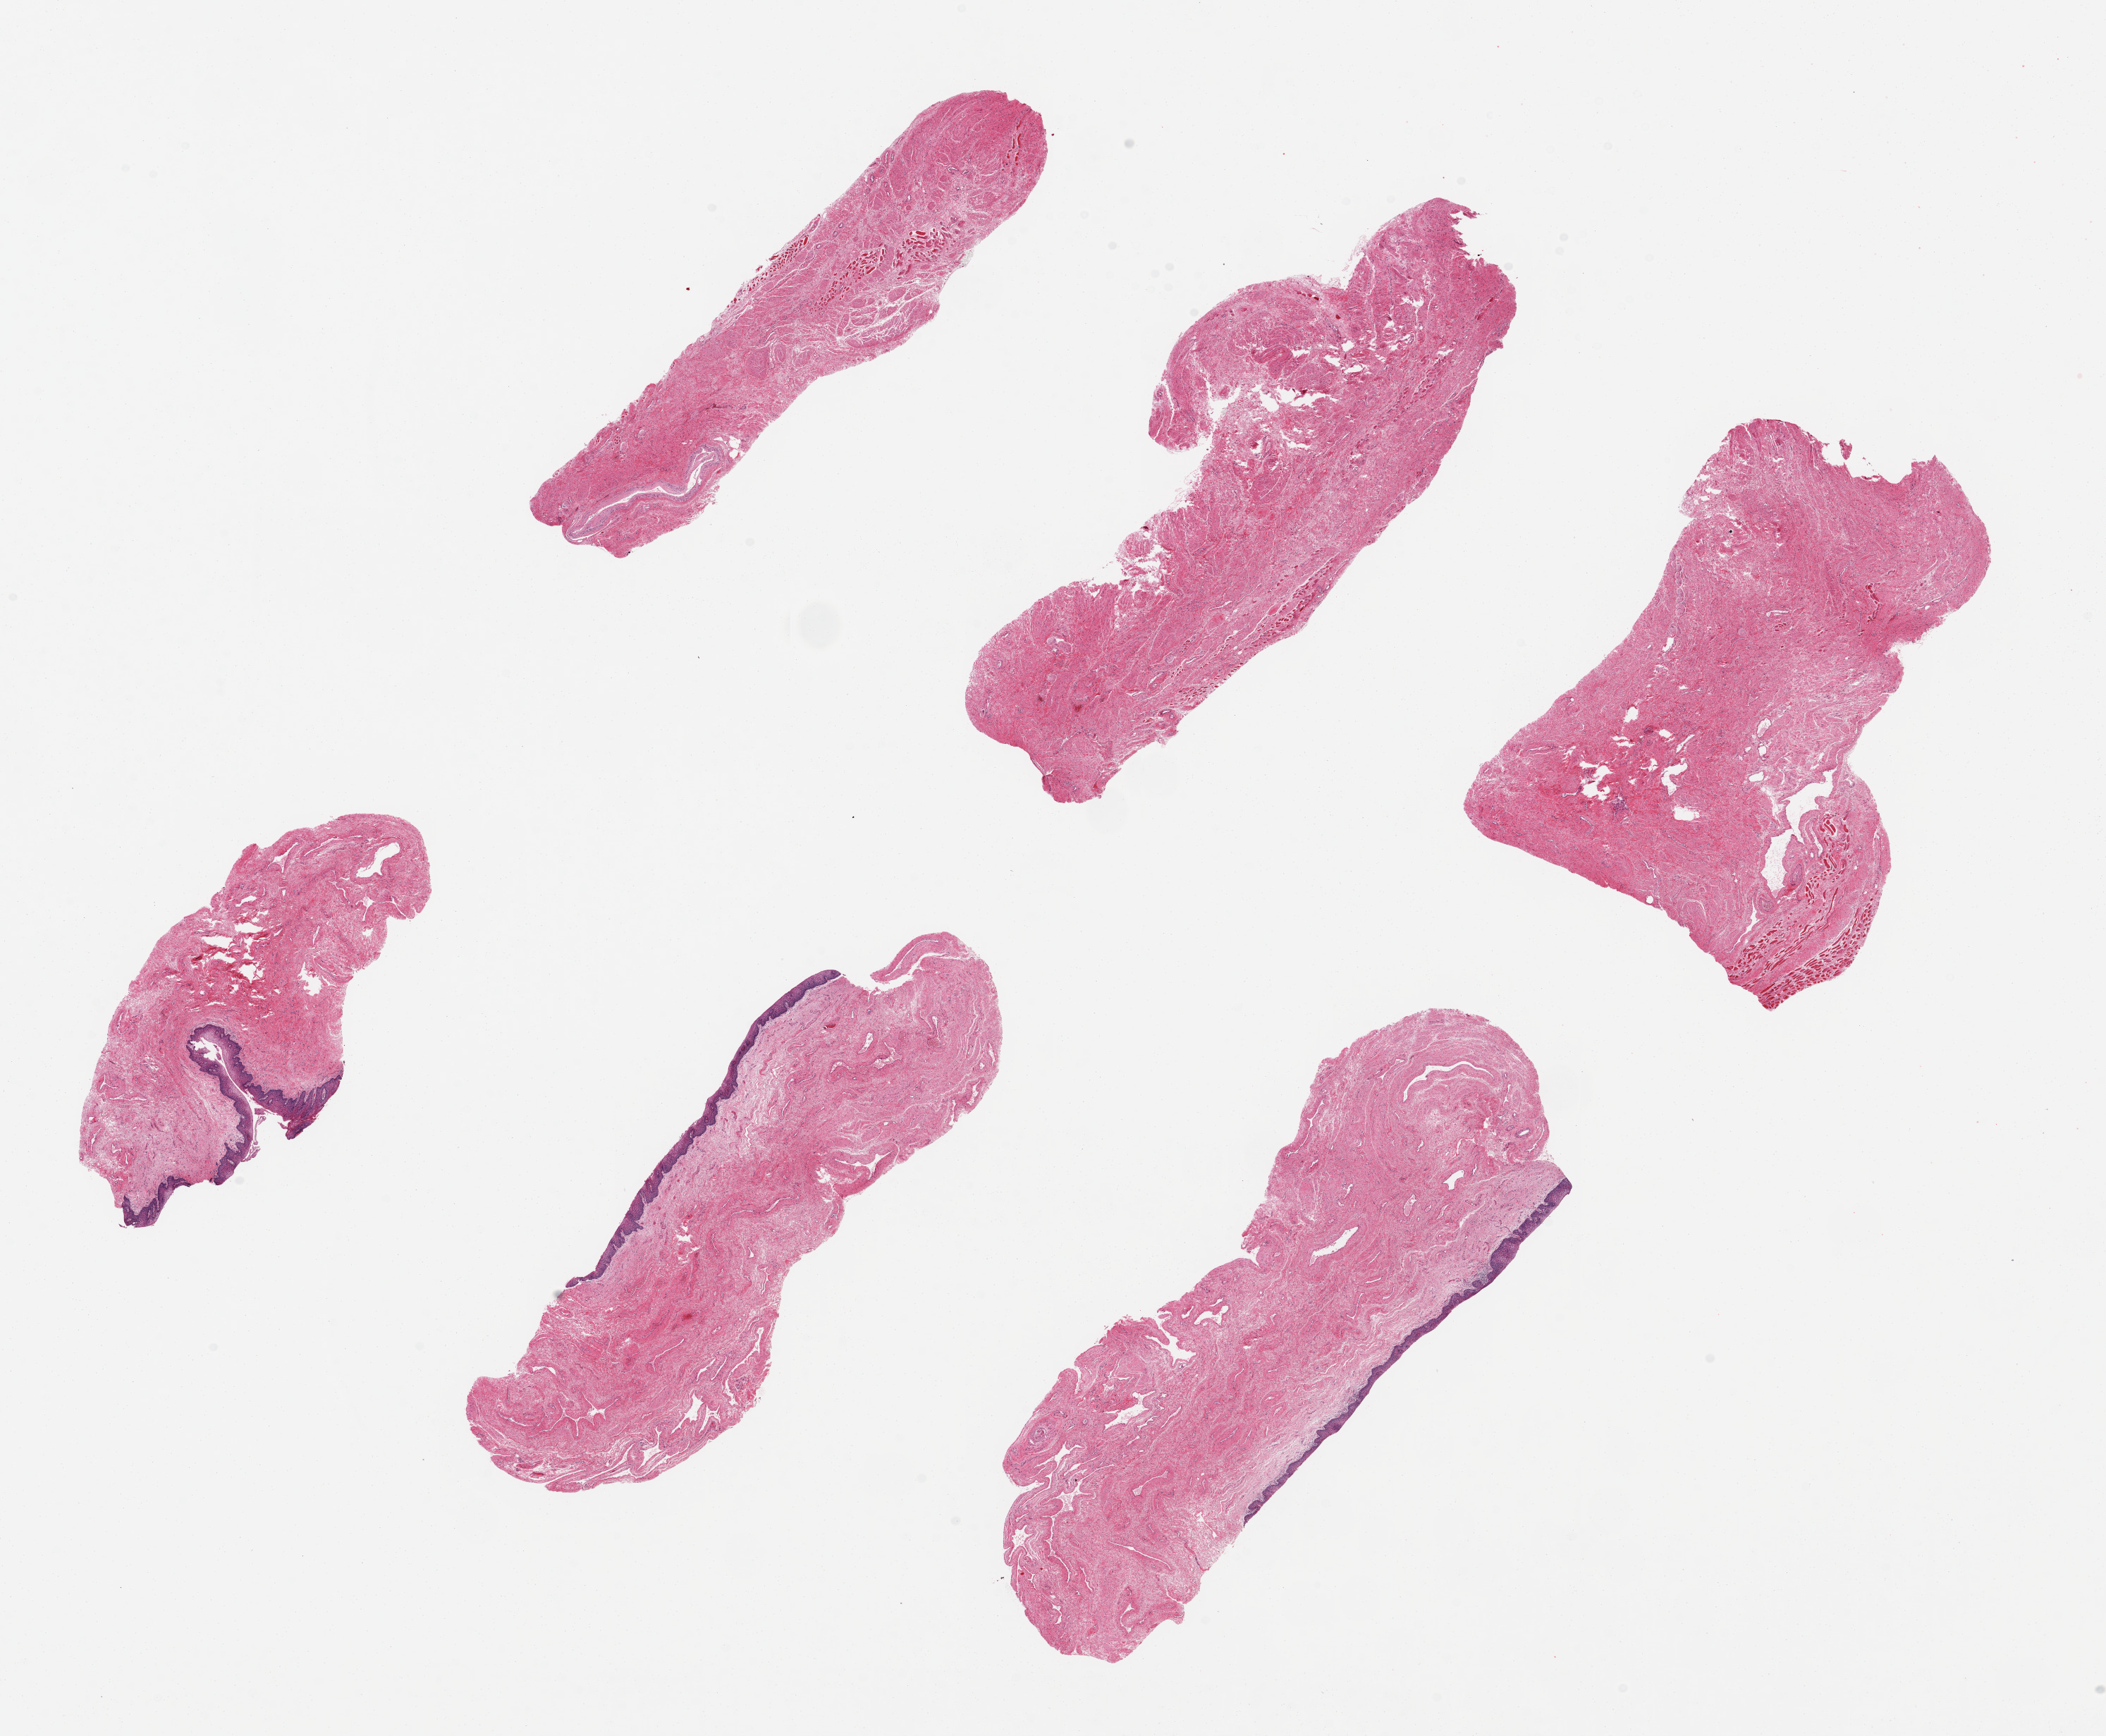
Digitized haematoxylin and eosin-stained section — whole scanned area (about 23.6 x 19.5 mm, acquisition: 20x scan) shown as a low-resolution overview. PAXgene-fixed paraffin-embedded (PFPE) section. Target tissue: vagina. Tissue donor sample. Donor: female.
- review note (as recorded): 6 pieces measuring up to 8x3 mm; well preserved squamous mucosa on 3 pieces; no mucosa on 3